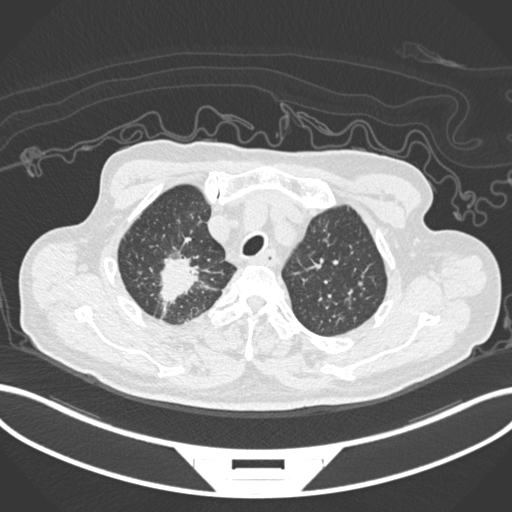
Chest CT, one axial slice. Position 179 of 207 along the scan axis. Reconstruction kernel B30f. 120 kVp. Lung window (W 1500 / L -600 HU). 512 × 512 image matrix, field of view 400 × 400 mm. Patient: male, 69 years. From the clinical record (not read from this slice): clinical TNM (as recorded): T1c N1 M1.
Annotated regions visible in this slice (bounding box drawn by a radiologist):
- lung tumour (recorded histology: adenocarcinoma): bounding box (x1, y1, x2, y2) in pixels: (152, 247, 212, 307)